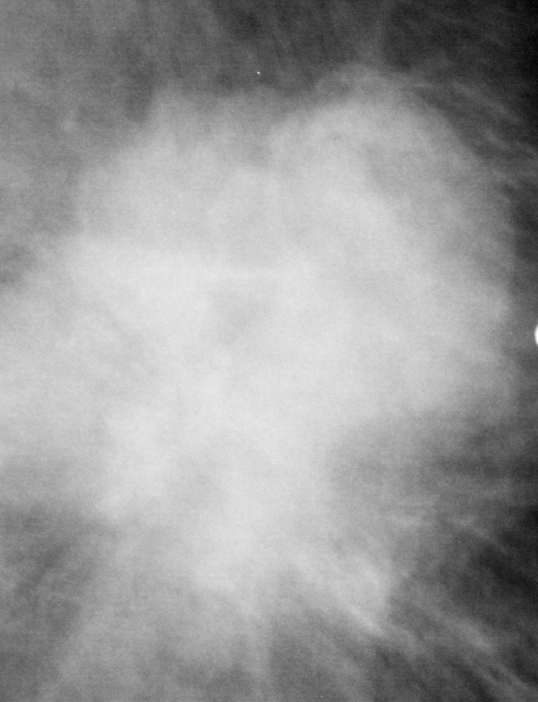
Region of interest cut from a scanned film mammogram (one marked finding), left breast, MLO view, BI-RADS breast density category 2 (scale 1–4).
- Marked abnormality: mass, shape irregular, margins spiculated; BI-RADS assessment category 5; subtlety rating 5 on a 1 (subtle) to 5 (obvious) scale; pathology (as recorded): malignant.